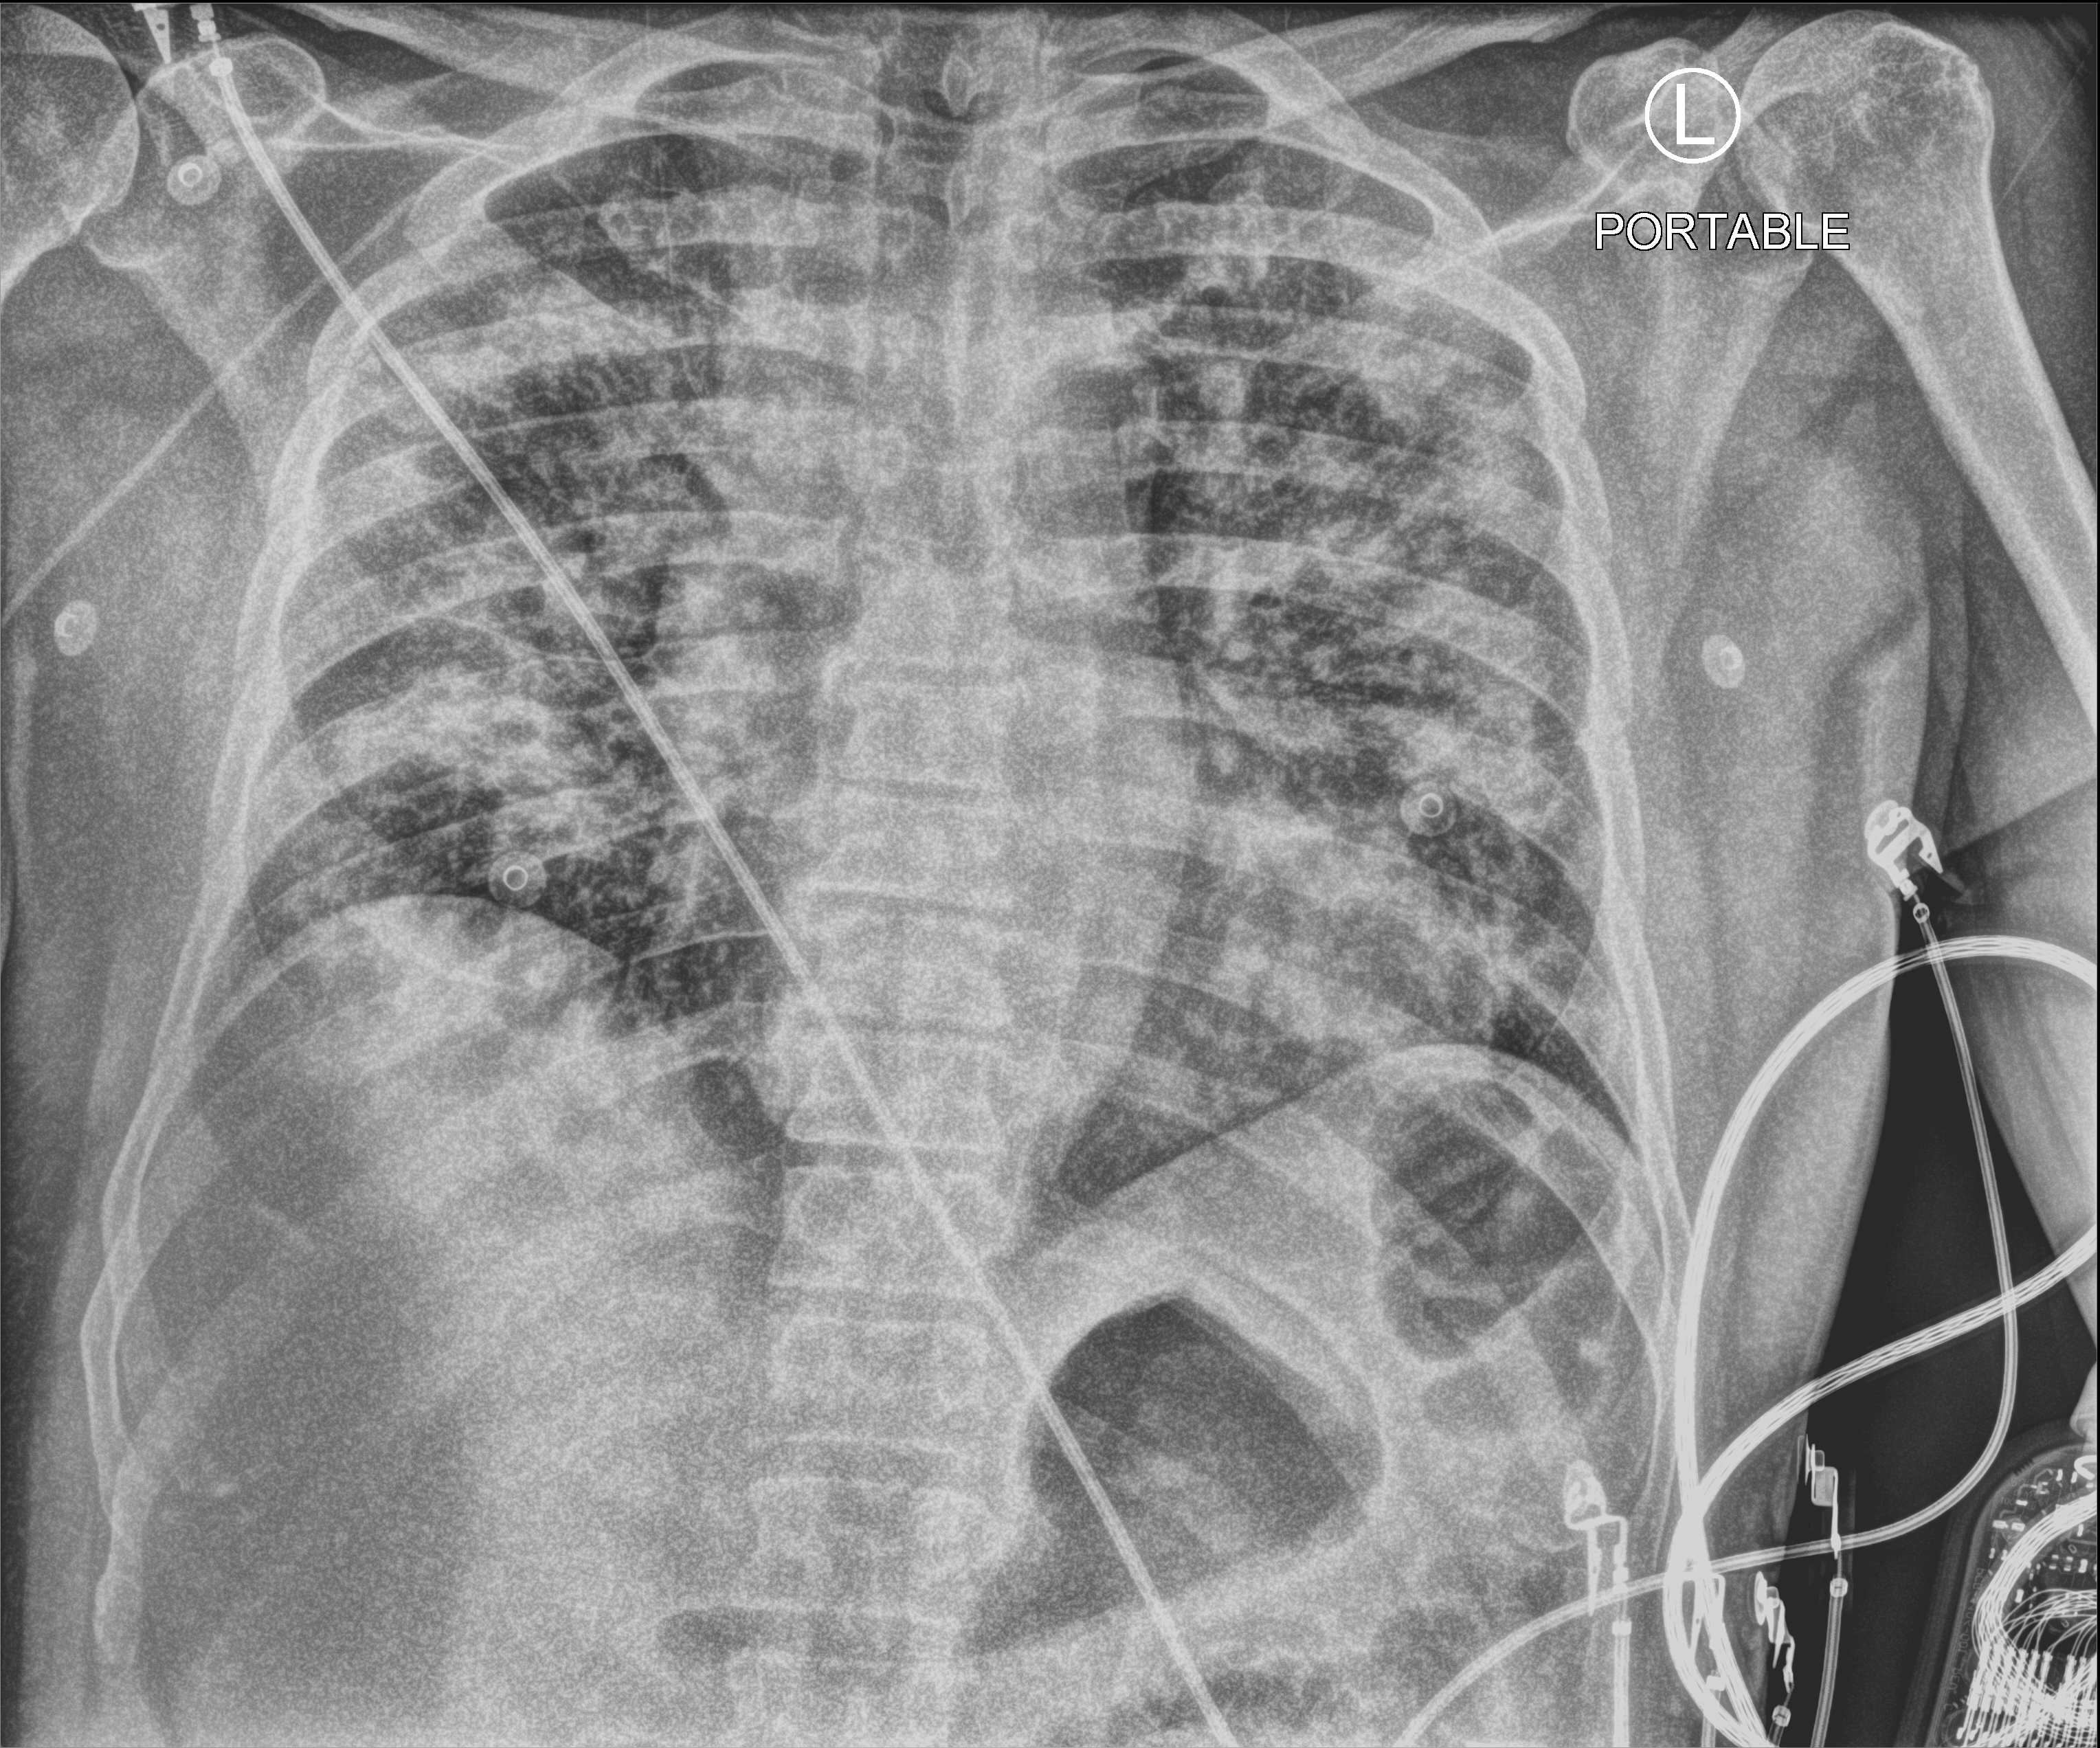
Portable chest radiograph. Patient hospitalised with COVID-19; male, aged 60–74 years.
Hospital-stay facts (about this admission, not read from this image; timing relative to this image not recorded): COPD (admission record): no.